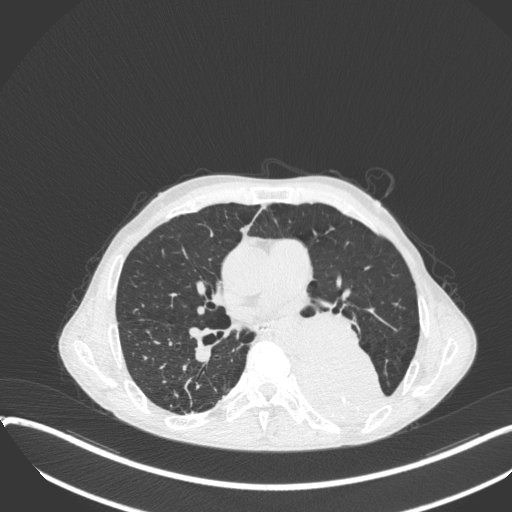
Chest CT, one axial slice; position 199 of 400 along the scan axis; 120 kVp; lung window (W 1500 / L -600 HU); 512 × 512 image matrix, field of view 400 × 400 mm. Patient: male, 57 years. Case-level facts recorded for this patient, not image findings: clinical TNM (as recorded): T4 N0 M0.
Structures marked on this image (bounding box drawn by a radiologist):
- lung tumour (recorded histology: squamous cell carcinoma): bounding box <286,335,393,426> (left, top, right, bottom; pixels)